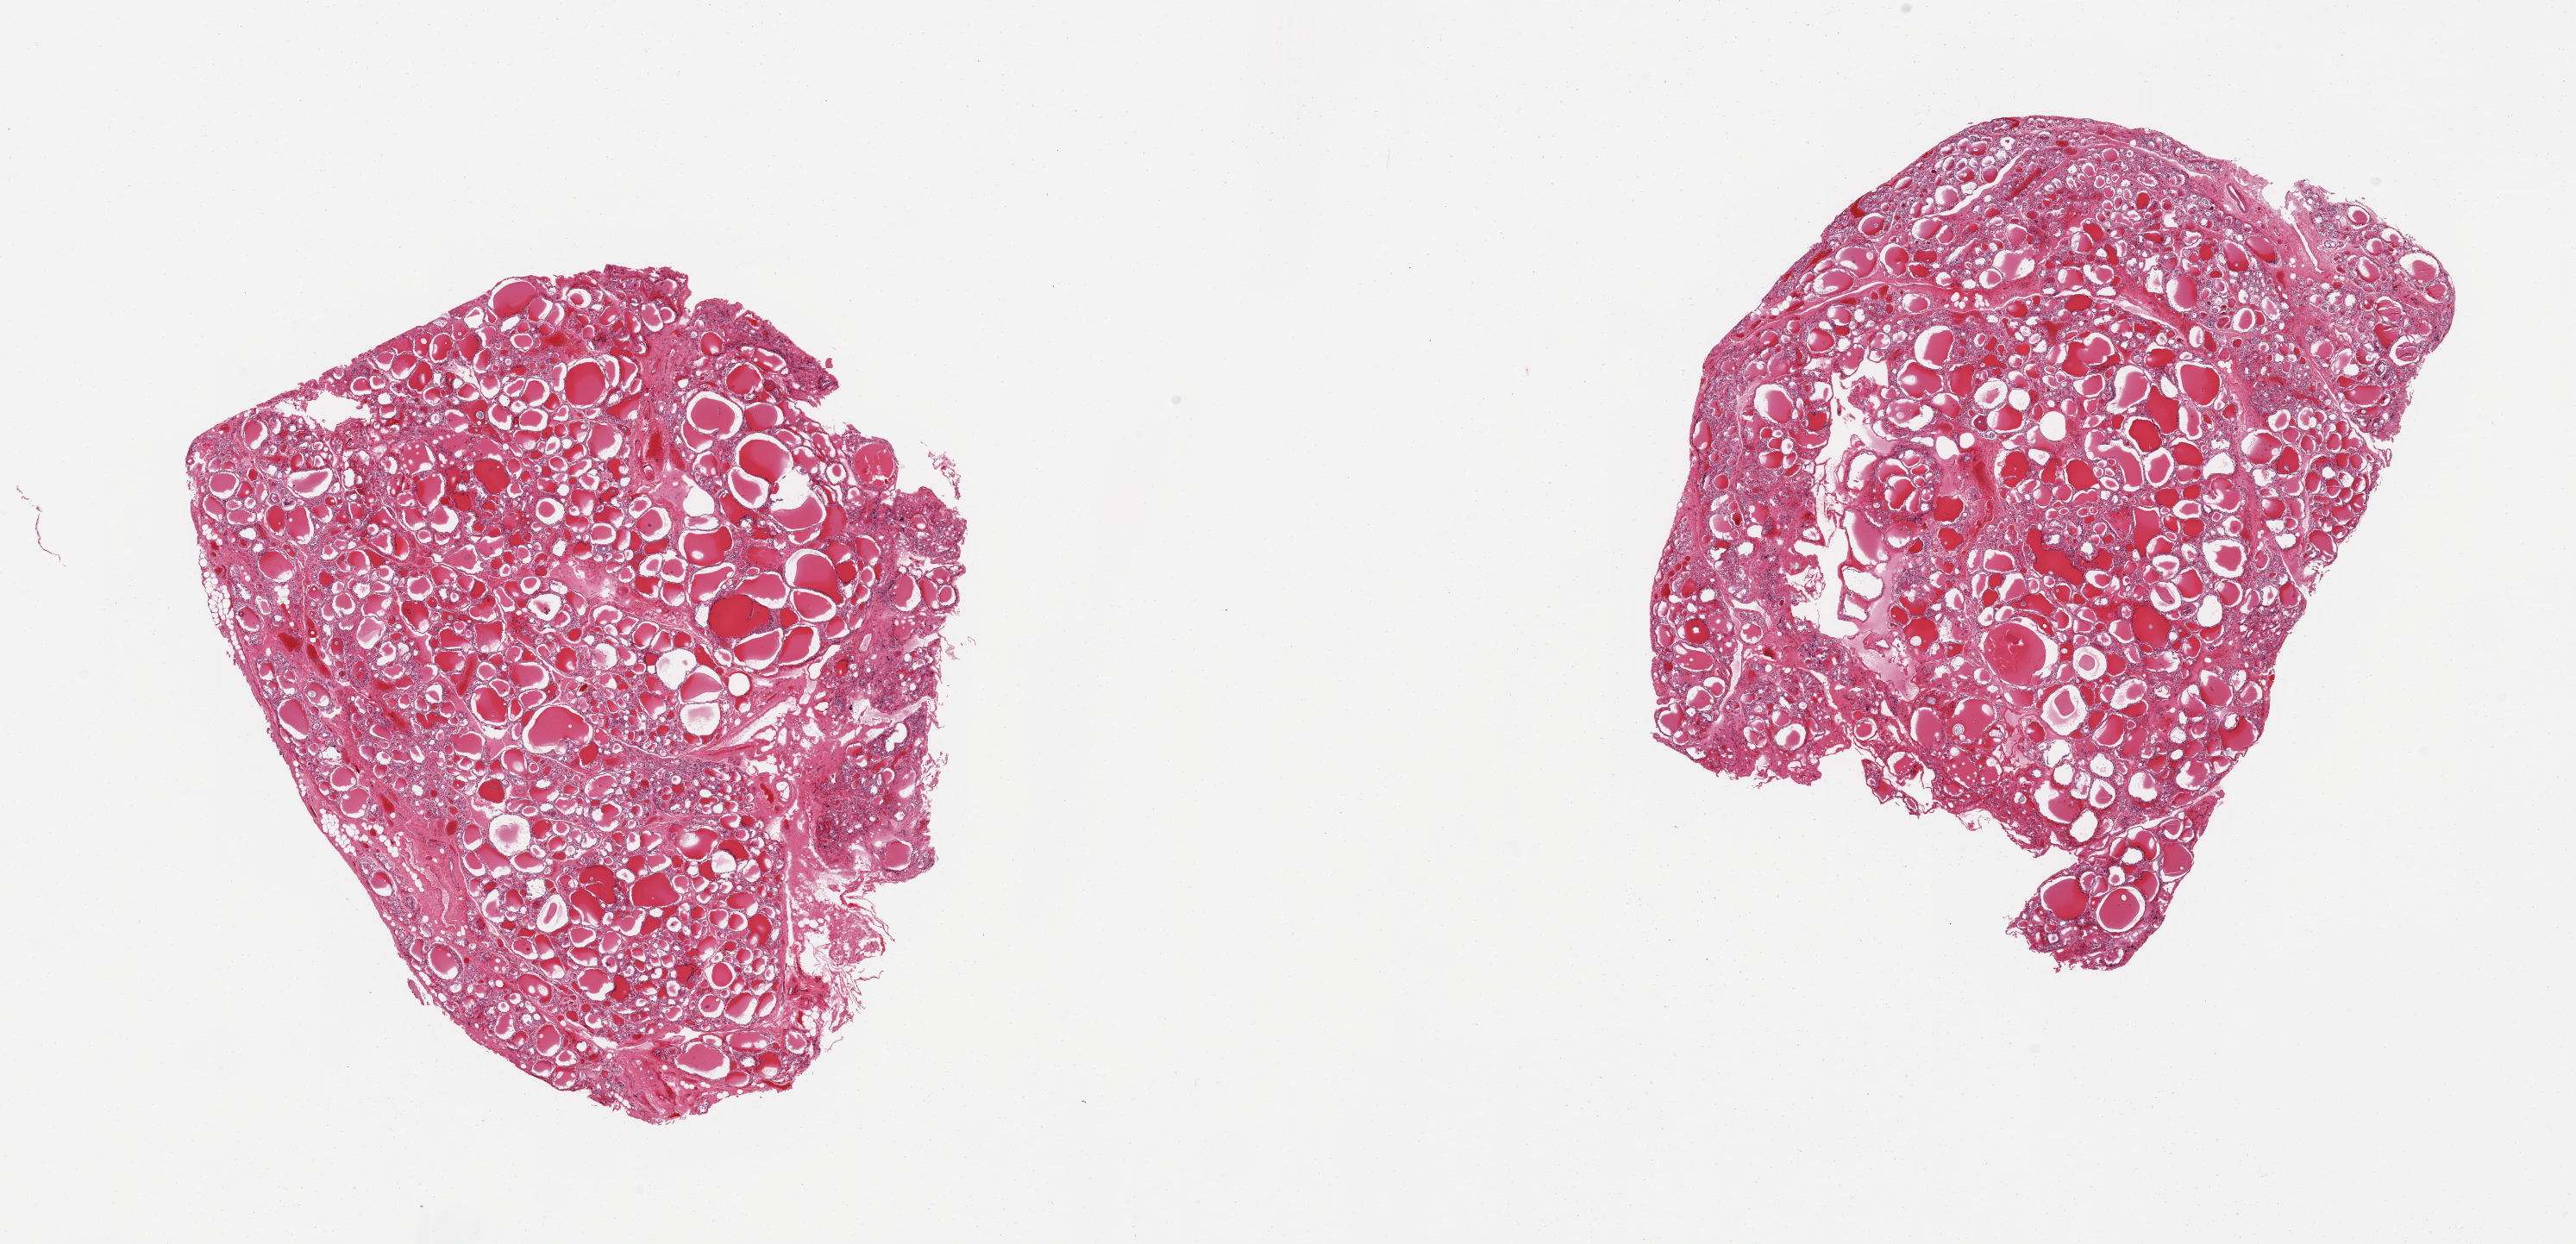
H&E whole-slide image, shown as a low-resolution overview of the whole scanned area (about 23.6 x 11.4 mm, from a 20x scan); PAXgene-fixed paraffin-embedded (PFPE) section; sampled site (target tissue): thyroid; tissue donor sample. Donor: female.
Reviewer comment on this tissue sample: 2 pieces, no abnormalities.